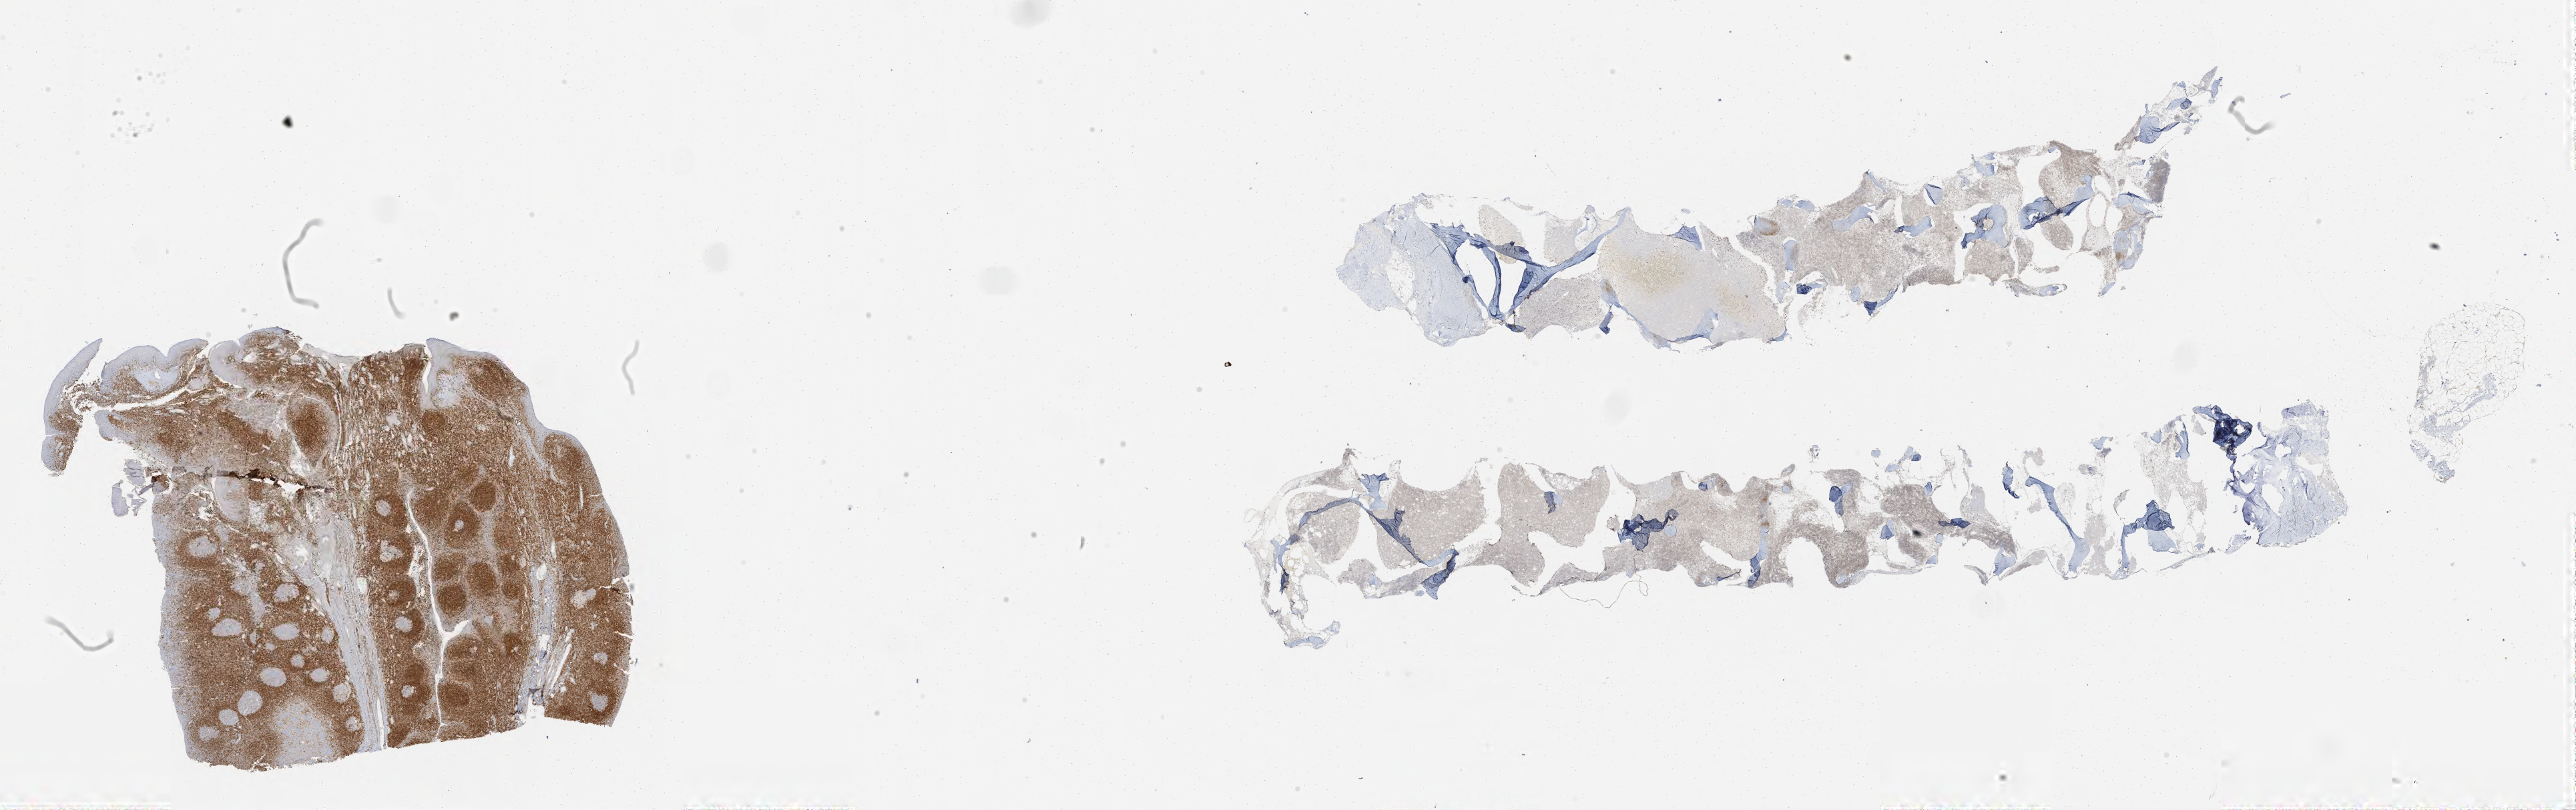
Whole-slide image, immunohistochemical stain for BCL2, a low-resolution overview of the entire scanned area, about 31.0 x 9.8 mm. Tumor tissue. Patient female; 60 years old.
Diagnosis: Burkitt lymphoma, NOS.